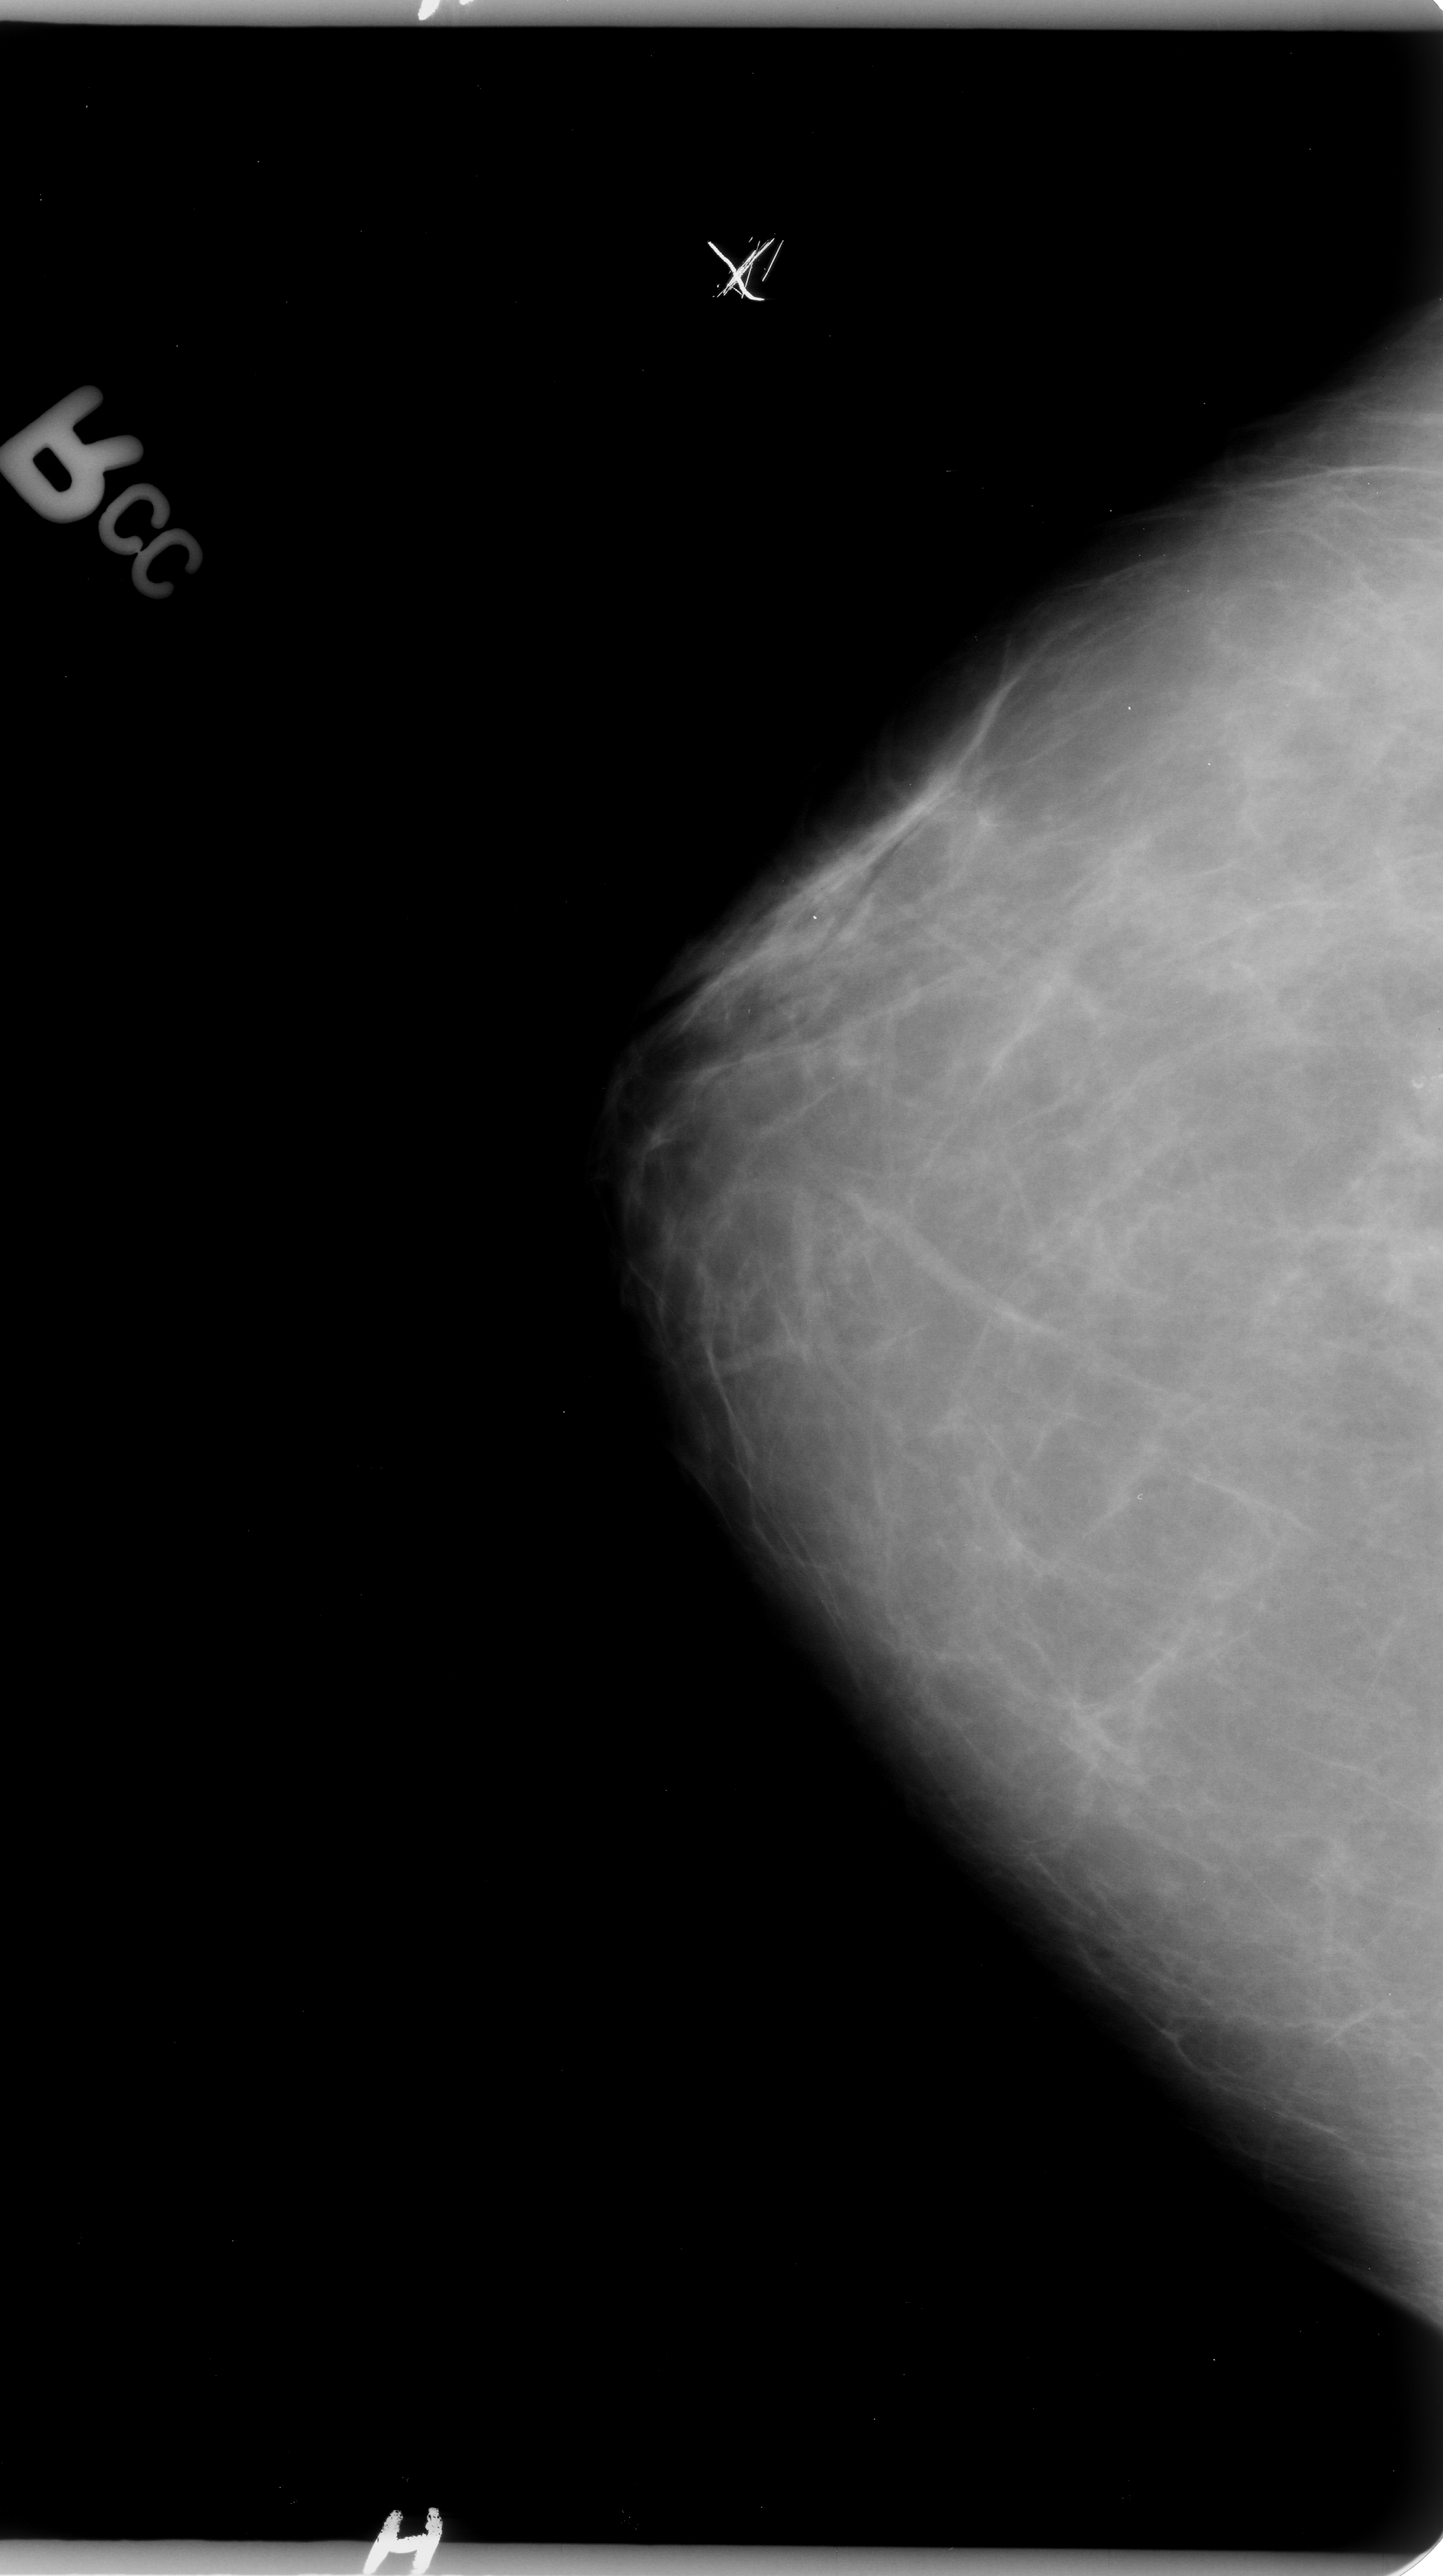
Digitized screen-film mammogram. Right breast. Craniocaudal (CC) view. BI-RADS breast density category 2 (scale 1–4). 1443 × 2576 image matrix.
Expert-marked regions of interest on this image (one box per marked abnormality):
- calcifications, morphology pleomorphic, distribution clustered; BI-RADS assessment category 4; subtlety rating 4 on a 1 (subtle) to 5 (obvious) scale; pathology (as recorded): malignant: bounding box <1368,966,1440,1138> (left, top, right, bottom; pixels)